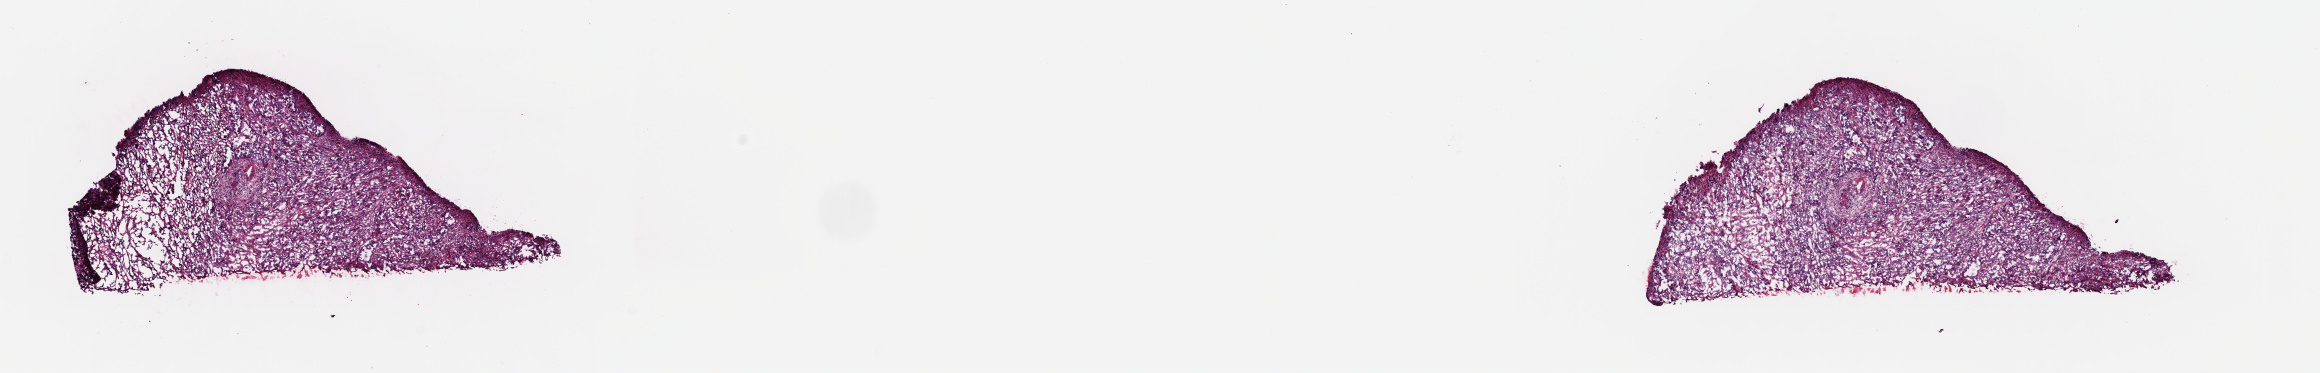
Digitized H&E-stained tissue section (whole slide), whole scanned area (about 18.3 x 2.9 mm, from a 40x scan) shown as a low-resolution overview; frozen section from the top of the tissue portion; primary tumour sample from the uterus. Female, age 80 years at initial diagnosis. Histologic grade: G3 (poorly differentiated). Slide review estimates, as recorded: tumour cells 80%, tumour nuclei 80%, normal cells 0%, stromal cells 15%, necrosis 5%. Infiltration values recorded for this section: lymphocyte infiltration 70%, monocyte infiltration 10%, neutrophil infiltration 10%.
- FIGO stage: IB
- pathologic diagnosis: Serous cystadenocarcinoma, NOS